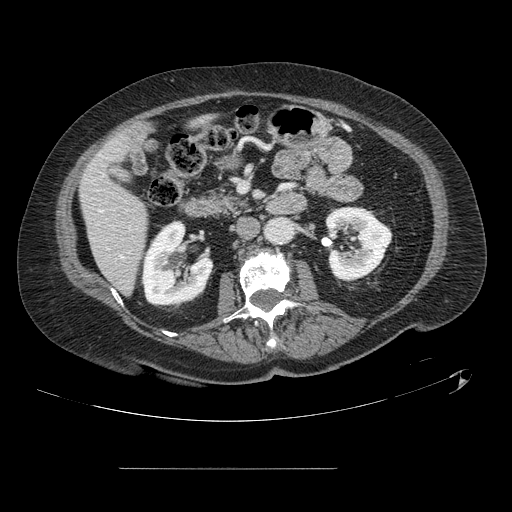
Contrast-enhanced abdominal CT, one axial slice. Slice 40 of 148 in the series (ordered by position). 120 kVp. Intravenous contrast given. Soft-tissue window (W 400 / L 40 HU). 2.5 mm slice thickness. 512 × 512 image matrix, field of view 439 × 439 mm. Female patient, age 75 years. Case-level facts recorded for this patient, not image findings: diagnosis: colorectal cancer liver metastases, imaged before liver resection; multiple liver metastases: no.
Outlined on this slice (outlined manually by an expert reader):
- hepatic veins: bounding box (x1, y1, x2, y2) in pixels: (101, 211, 124, 259)
- liver: (81, 135, 148, 294)
- planned liver remnant (the part of the liver to remain after resection): (81, 135, 148, 294)